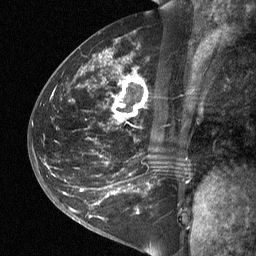
Breast MRI (dynamic contrast-enhanced), one sagittal slice; position 31 of 64 along the scan axis; dynamic contrast-enhanced study with each time point stored as its own series, time point 2 of 3 at this slice position (early post-contrast, ordered by acquisition time); 1.5 T; TE 4.8 ms, TR 27 ms; 2 mm slice thickness; 256 × 256 image matrix, field of view 200 × 200 mm. Female patient, age 42 years. Case-level facts recorded for this patient, not image findings: setting: breast cancer imaged before/during neoadjuvant chemotherapy; receptor status: triple-negative.
Structures marked on this image (semi-automatic segmentation, software-assisted and operator-edited):
- analysis volume of interest (the breast-tissue region the enhancement analysis was run in; not a lesion): box from (x=49, y=45) to (x=197, y=197) px
- tumour enhancement mask (voxels above the 90 % enhancement threshold inside the analysis volume of interest): (x=117, y=79)–(x=142, y=105)